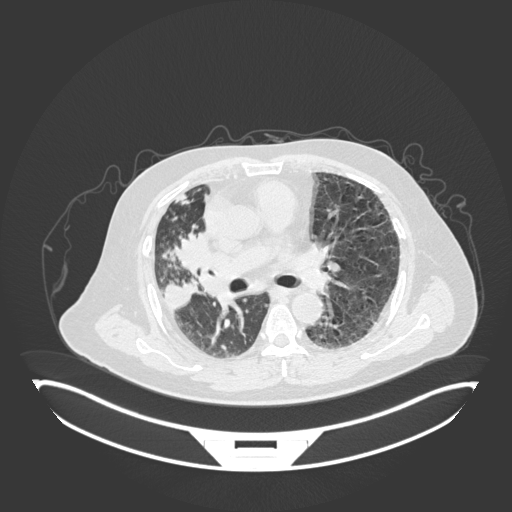
Chest CT, one axial slice; reconstruction kernel B30f; lung window (W 1500 / L -600 HU); 1 mm slice thickness; 512 × 512 image matrix, field of view 500 × 500 mm. Male patient, age 69 years. From the clinical record (not read from this slice): clinical TNM (as recorded): T4 N3 M1.
Annotated regions visible in this slice (rectangle marked by the reading radiologist):
- lung tumour (recorded histology: adenocarcinoma): bounding box [x1, y1, x2, y2] px = [169, 230, 213, 279]